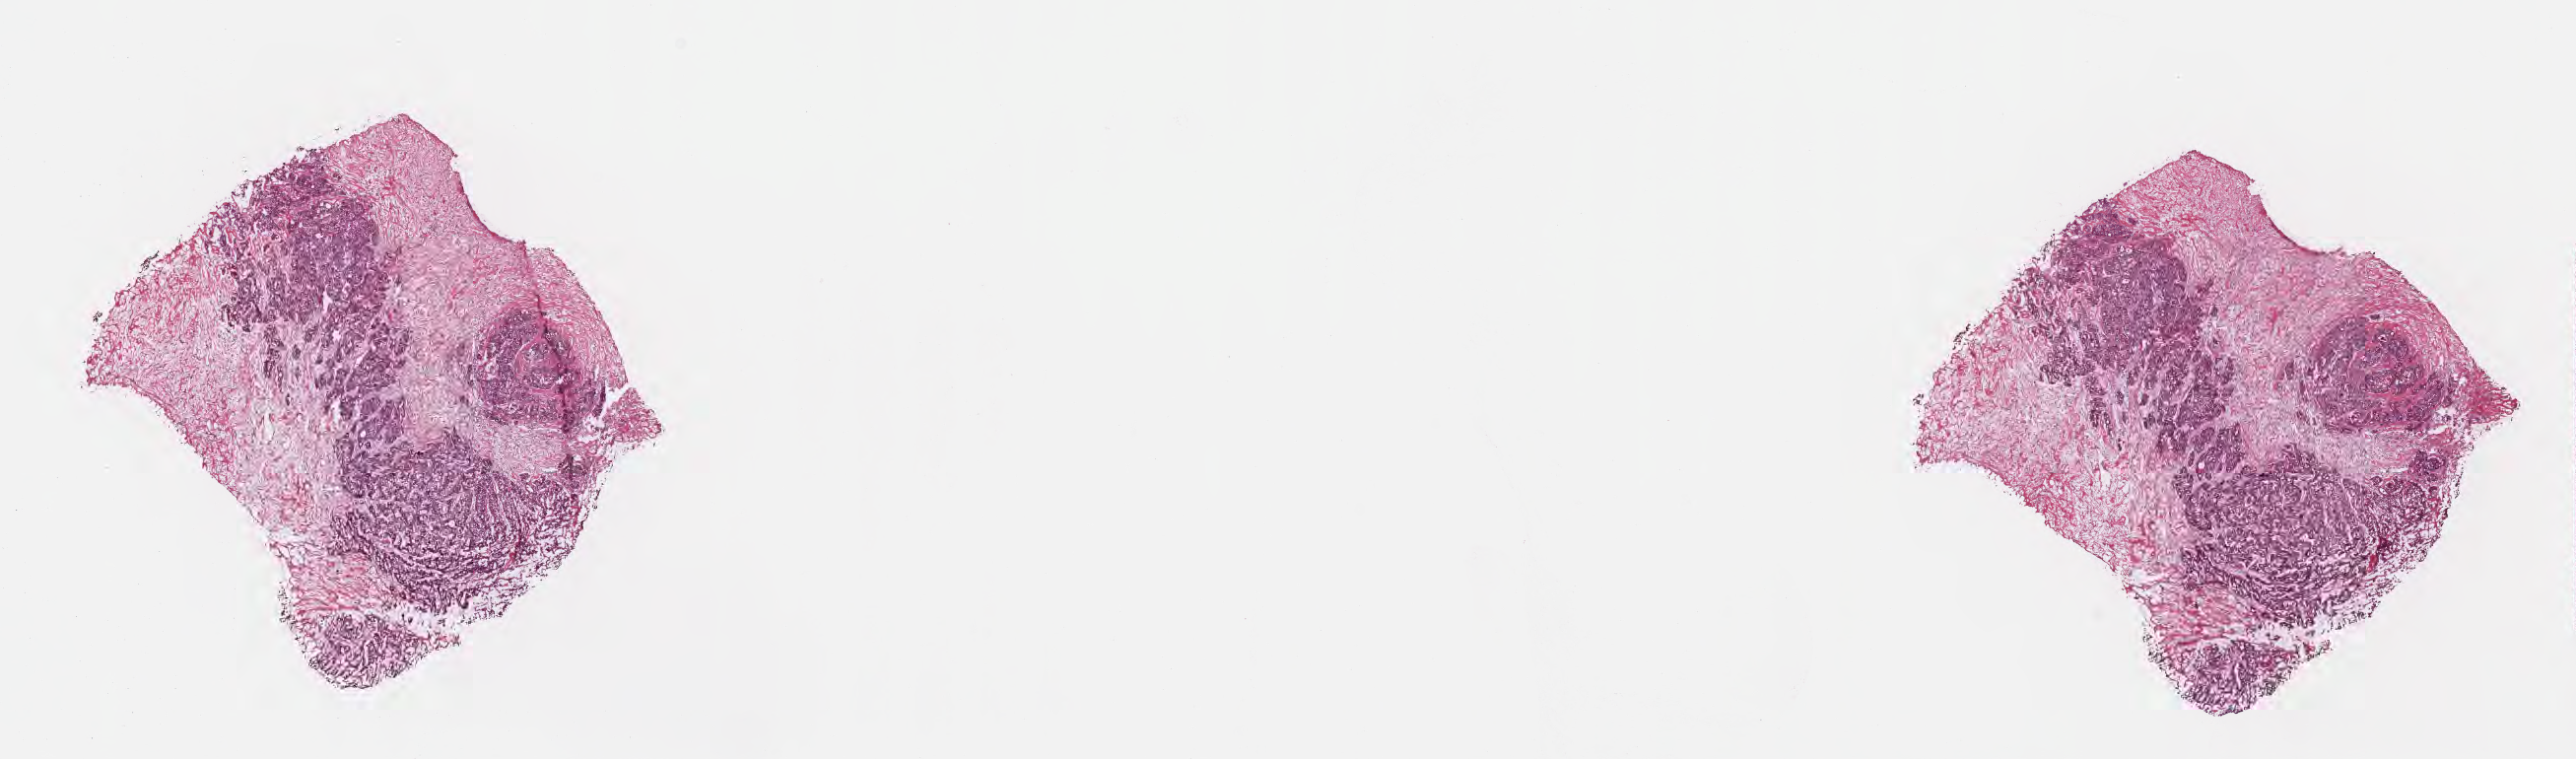
Hematoxylin and eosin (H&E) whole-slide image — whole scanned area (about 21.1 x 6.2 mm) shown as a low-resolution overview. Frozen section. Metastatic tumor tissue, resected from lymph node. Patient: female, age at initial diagnosis 76 years. Slide review estimates, as recorded: tumor cells 50%, tumor nuclei 60%, stromal cells 50%, necrosis 0%, normal cells 0%. Infiltration values recorded for this section: lymphocyte infiltration 0%, monocyte infiltration 0%, neutrophil infiltration 0%.
- patient diagnosis (primary): Adenocarcinoma, metastatic, NOS